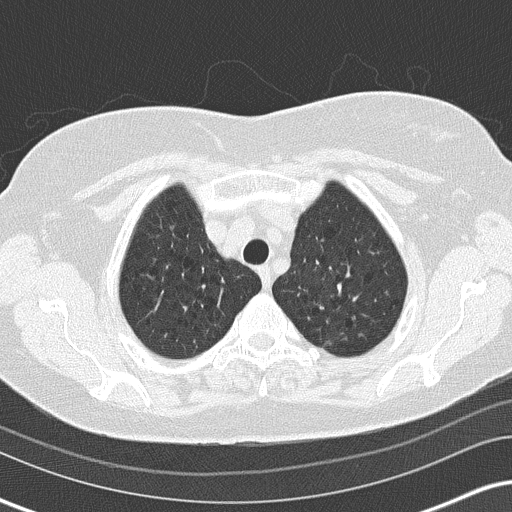
Low-dose screening chest CT, axial slice, first (baseline) screen, lung window (W 1500 / L -600 HU), 2 mm slice thickness, 512 × 512 image matrix. Female, age 65 years at enrolment. Former smoker at enrolment.
Expert-annotated lung lesion, box from (x=306, y=328) to (x=345, y=359) px. The exam's reader record, not a measurement of the box and not confirmed to be the same lesion: non-calcified nodule or mass ≥4 mm, left upper lobe, 6 × 5 mm, soft tissue attenuation. Lung cancer was diagnosed 800 days after this screen (after the third annual screen): adenocarcinoma, NOS, left upper lobe, moderately differentiated (G2), stage IA (AJCC 6th edition), 8 mm at pathology.